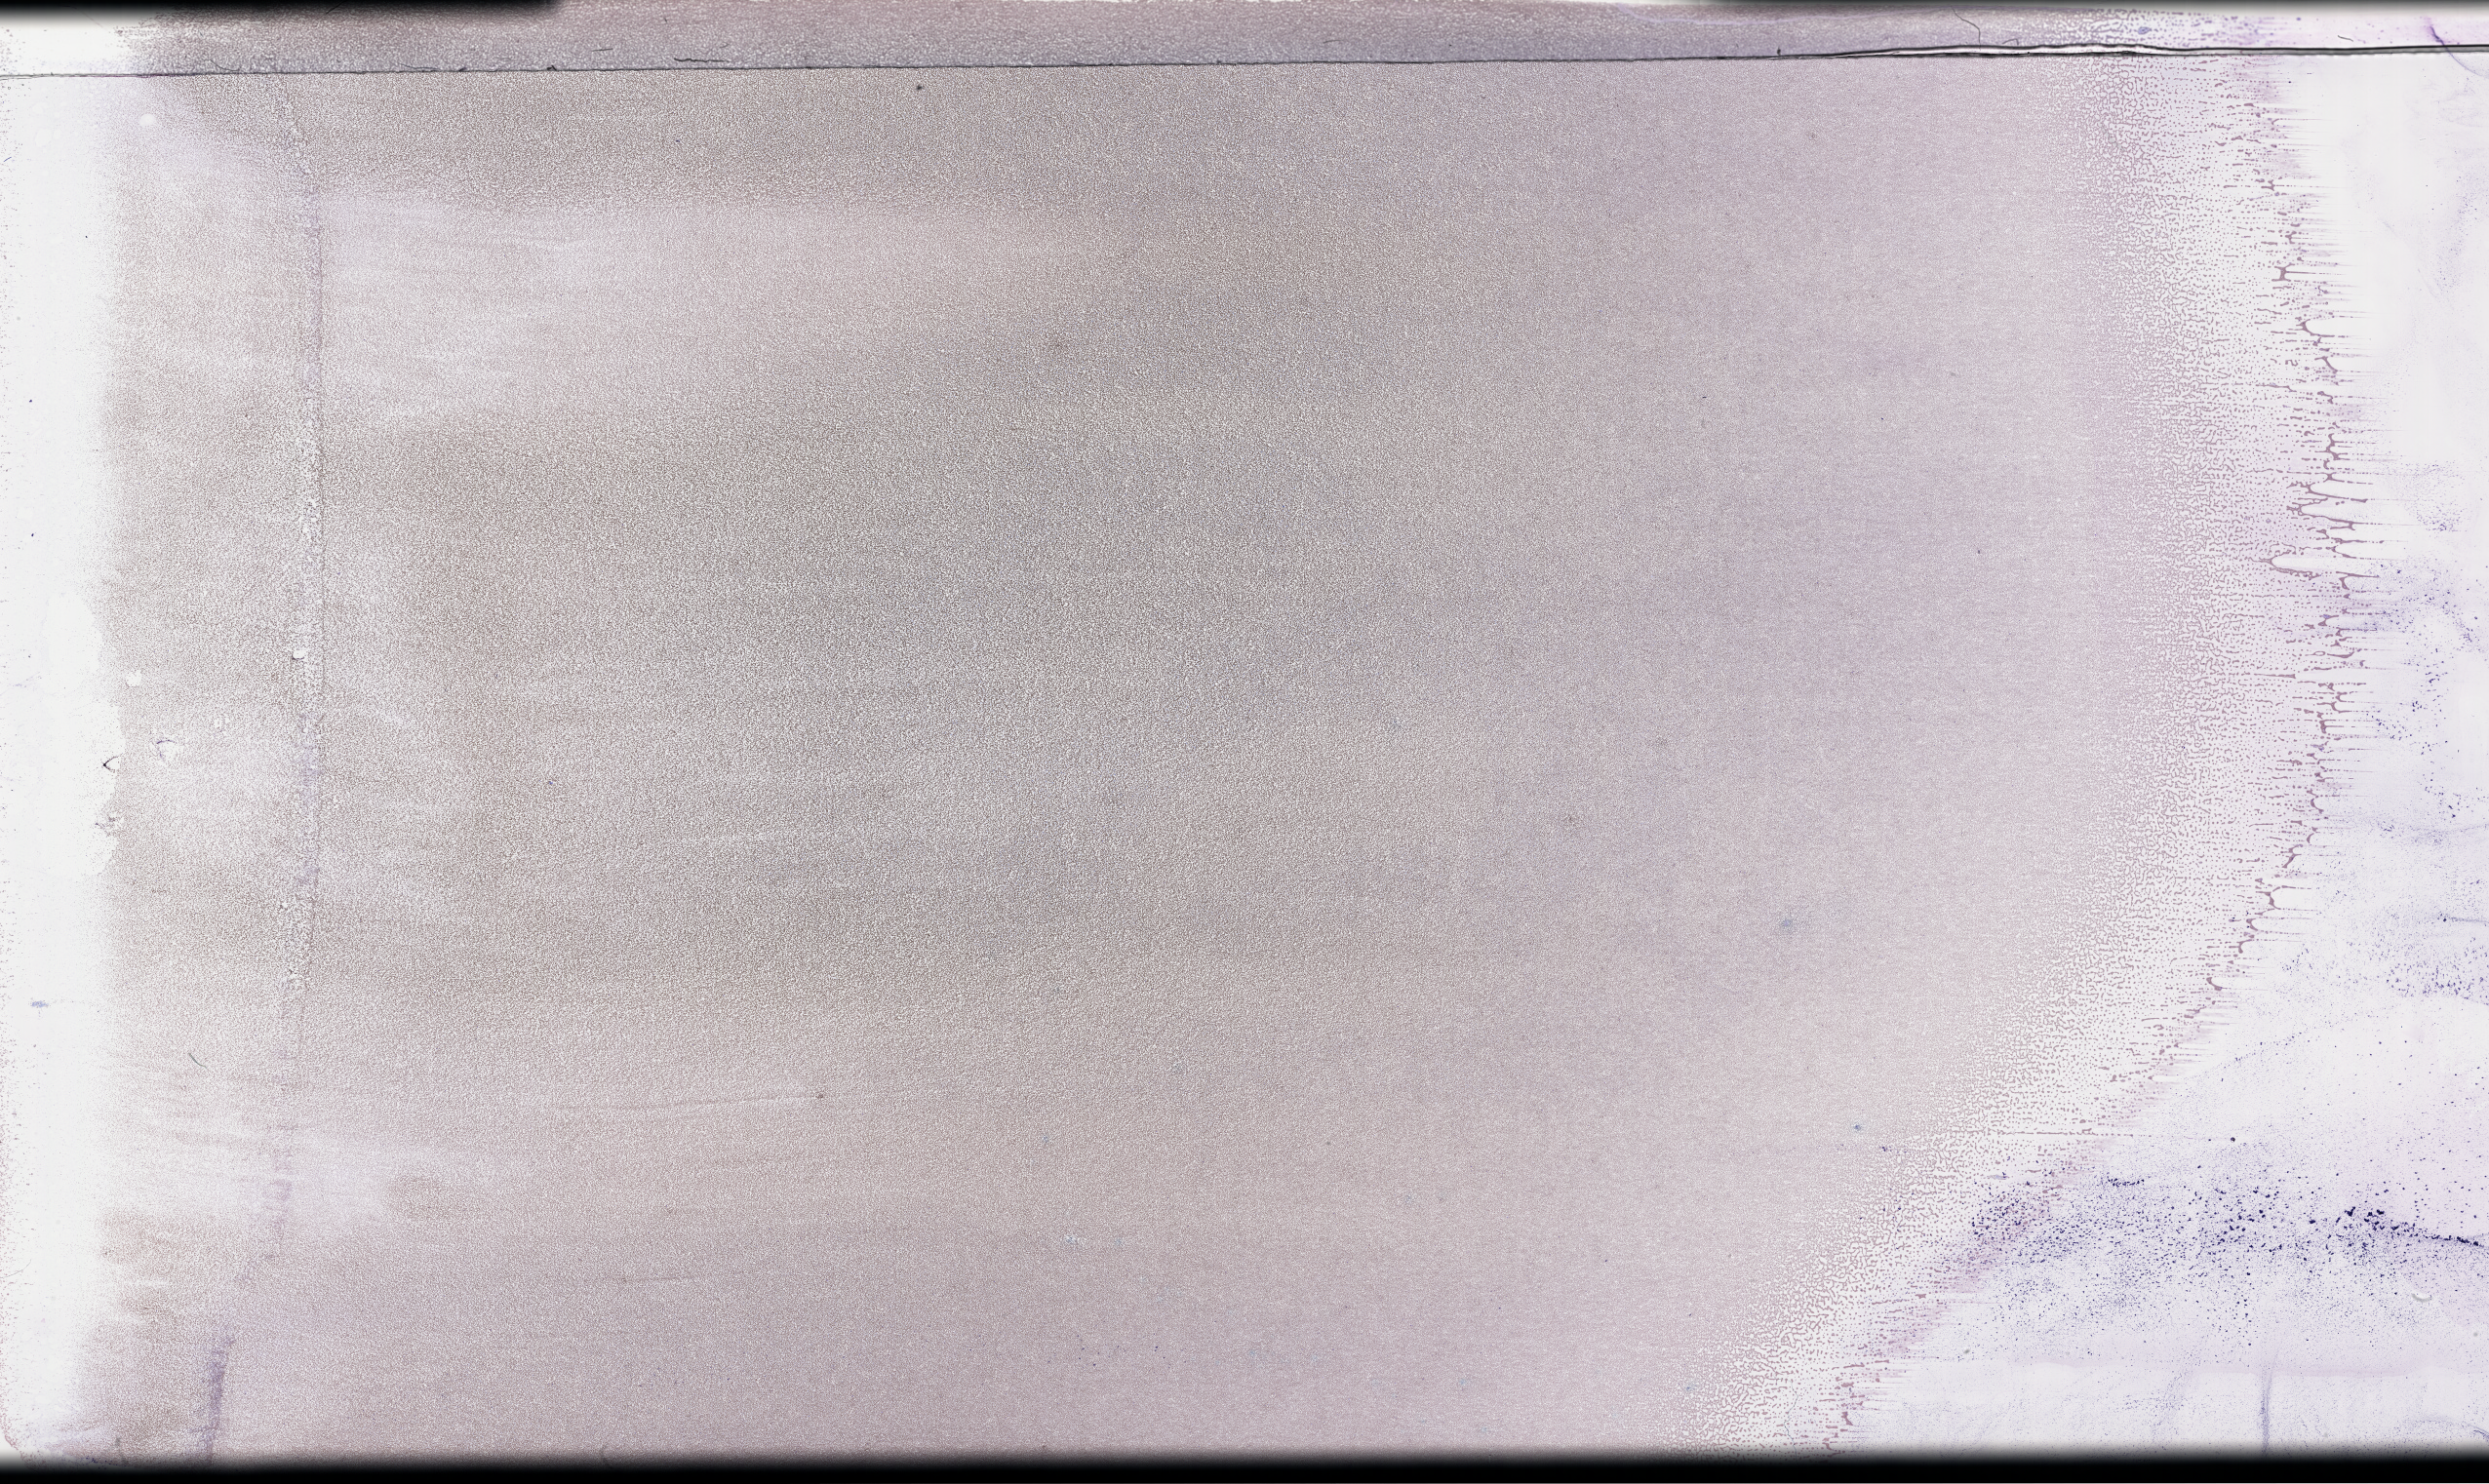
Wright–Giemsa-stained whole blood smear, whole-slide image, shown as a low-resolution overview of the whole scanned area (about 41.2 x 24.6 mm), collected post-treatment, no progression. Patient: female.
- patient diagnosis: Acute Myeloid Leukemia Not Otherwise Specified